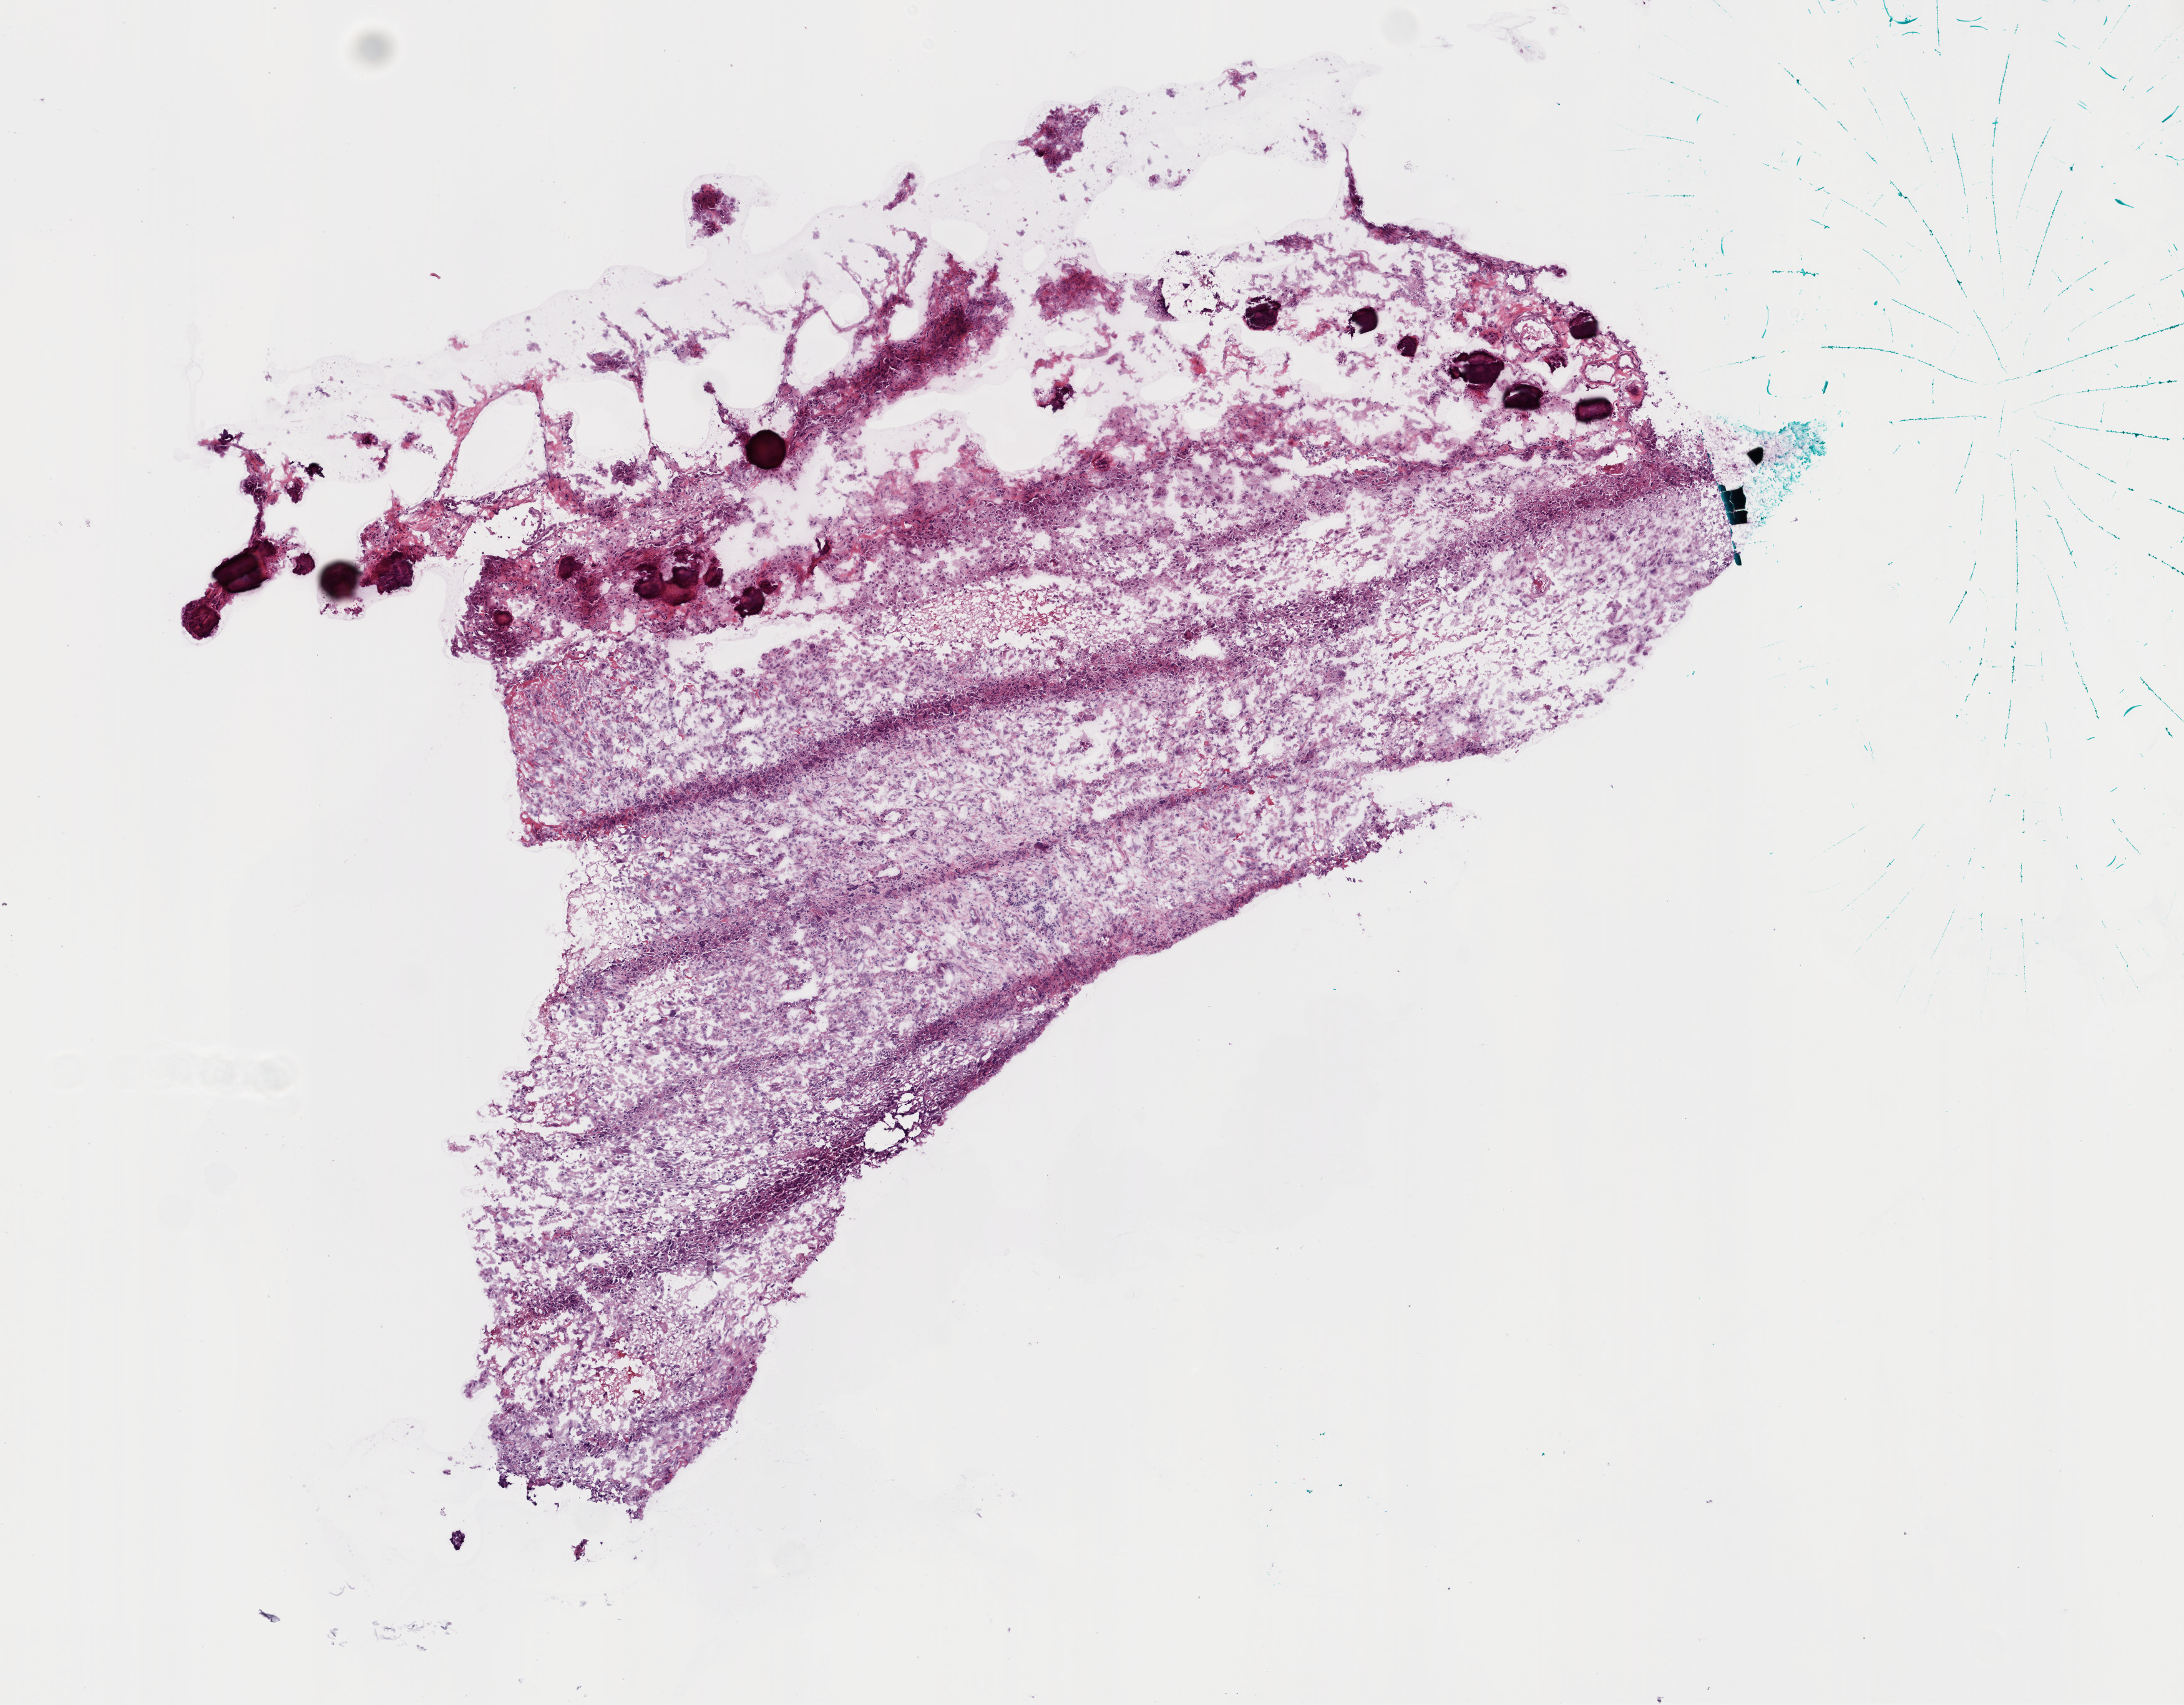
Digitized Hematoxylin and eosin (H&E) stained tissue section (whole slide), whole scanned area (about 7.0 x 5.5 mm) shown as a low-resolution overview. Frozen section. Primary tumour sample from the brain. Male, age 69 years at initial diagnosis. Slide review estimates, as recorded: tumour cells 80%, tumour nuclei 90%, normal cells 0%, stromal cells 5%, necrosis 15%. Inflammatory infiltration, as recorded: lymphocyte infiltration 90%, monocyte infiltration 0%, neutrophil infiltration 0%.
* pathologic diagnosis: Glioblastoma